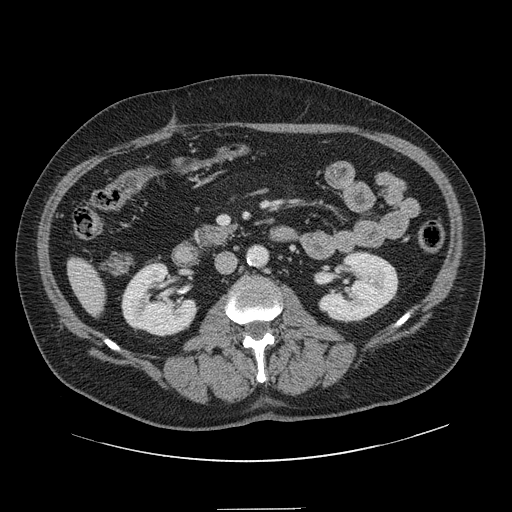
Contrast-enhanced abdominal CT, one axial slice; slice 38 of 154 in the series (ordered by position); 120 kVp; intravenous contrast given; soft-tissue window (W 400 / L 40 HU); 2.5 mm slice thickness; 512 × 512 image matrix, field of view 451 × 451 mm. Male patient, age 61 years. Case-level facts recorded for this patient, not image findings: diagnosis: colorectal cancer liver metastases, imaged before liver resection; multiple liver metastases: yes; largest metastasis: 2.6 cm; disease in both lobes: yes.
Structures marked on this image (outlined manually by an expert reader):
- liver: box from (x=69, y=260) to (x=106, y=315) px
- planned liver remnant (the part of the liver to remain after resection): (x=69, y=258)–(x=106, y=315)